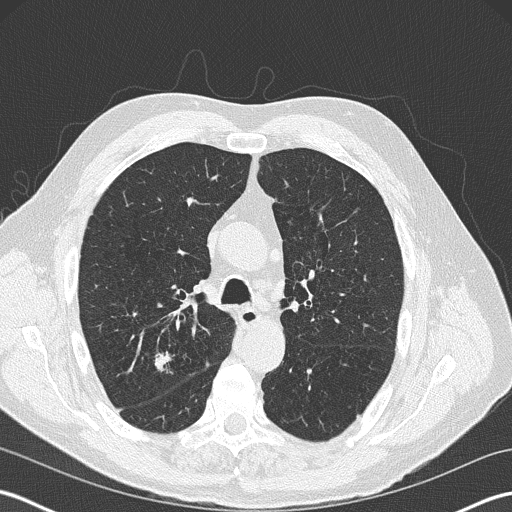
Low-dose screening chest CT, one axial slice. Slice 129 of 199 in the series (ordered by position). Reconstruction kernel B50f. 120 kVp. Lung window (W 1500 / L -600 HU). 2 mm slice thickness. 512 × 512 image matrix.
Structures marked on this image (outlined manually by an expert reader):
- lesion 1 (tumor, upper lobe of right lung): bounding box (x1, y1, x2, y2) in pixels: (154, 355, 167, 367)